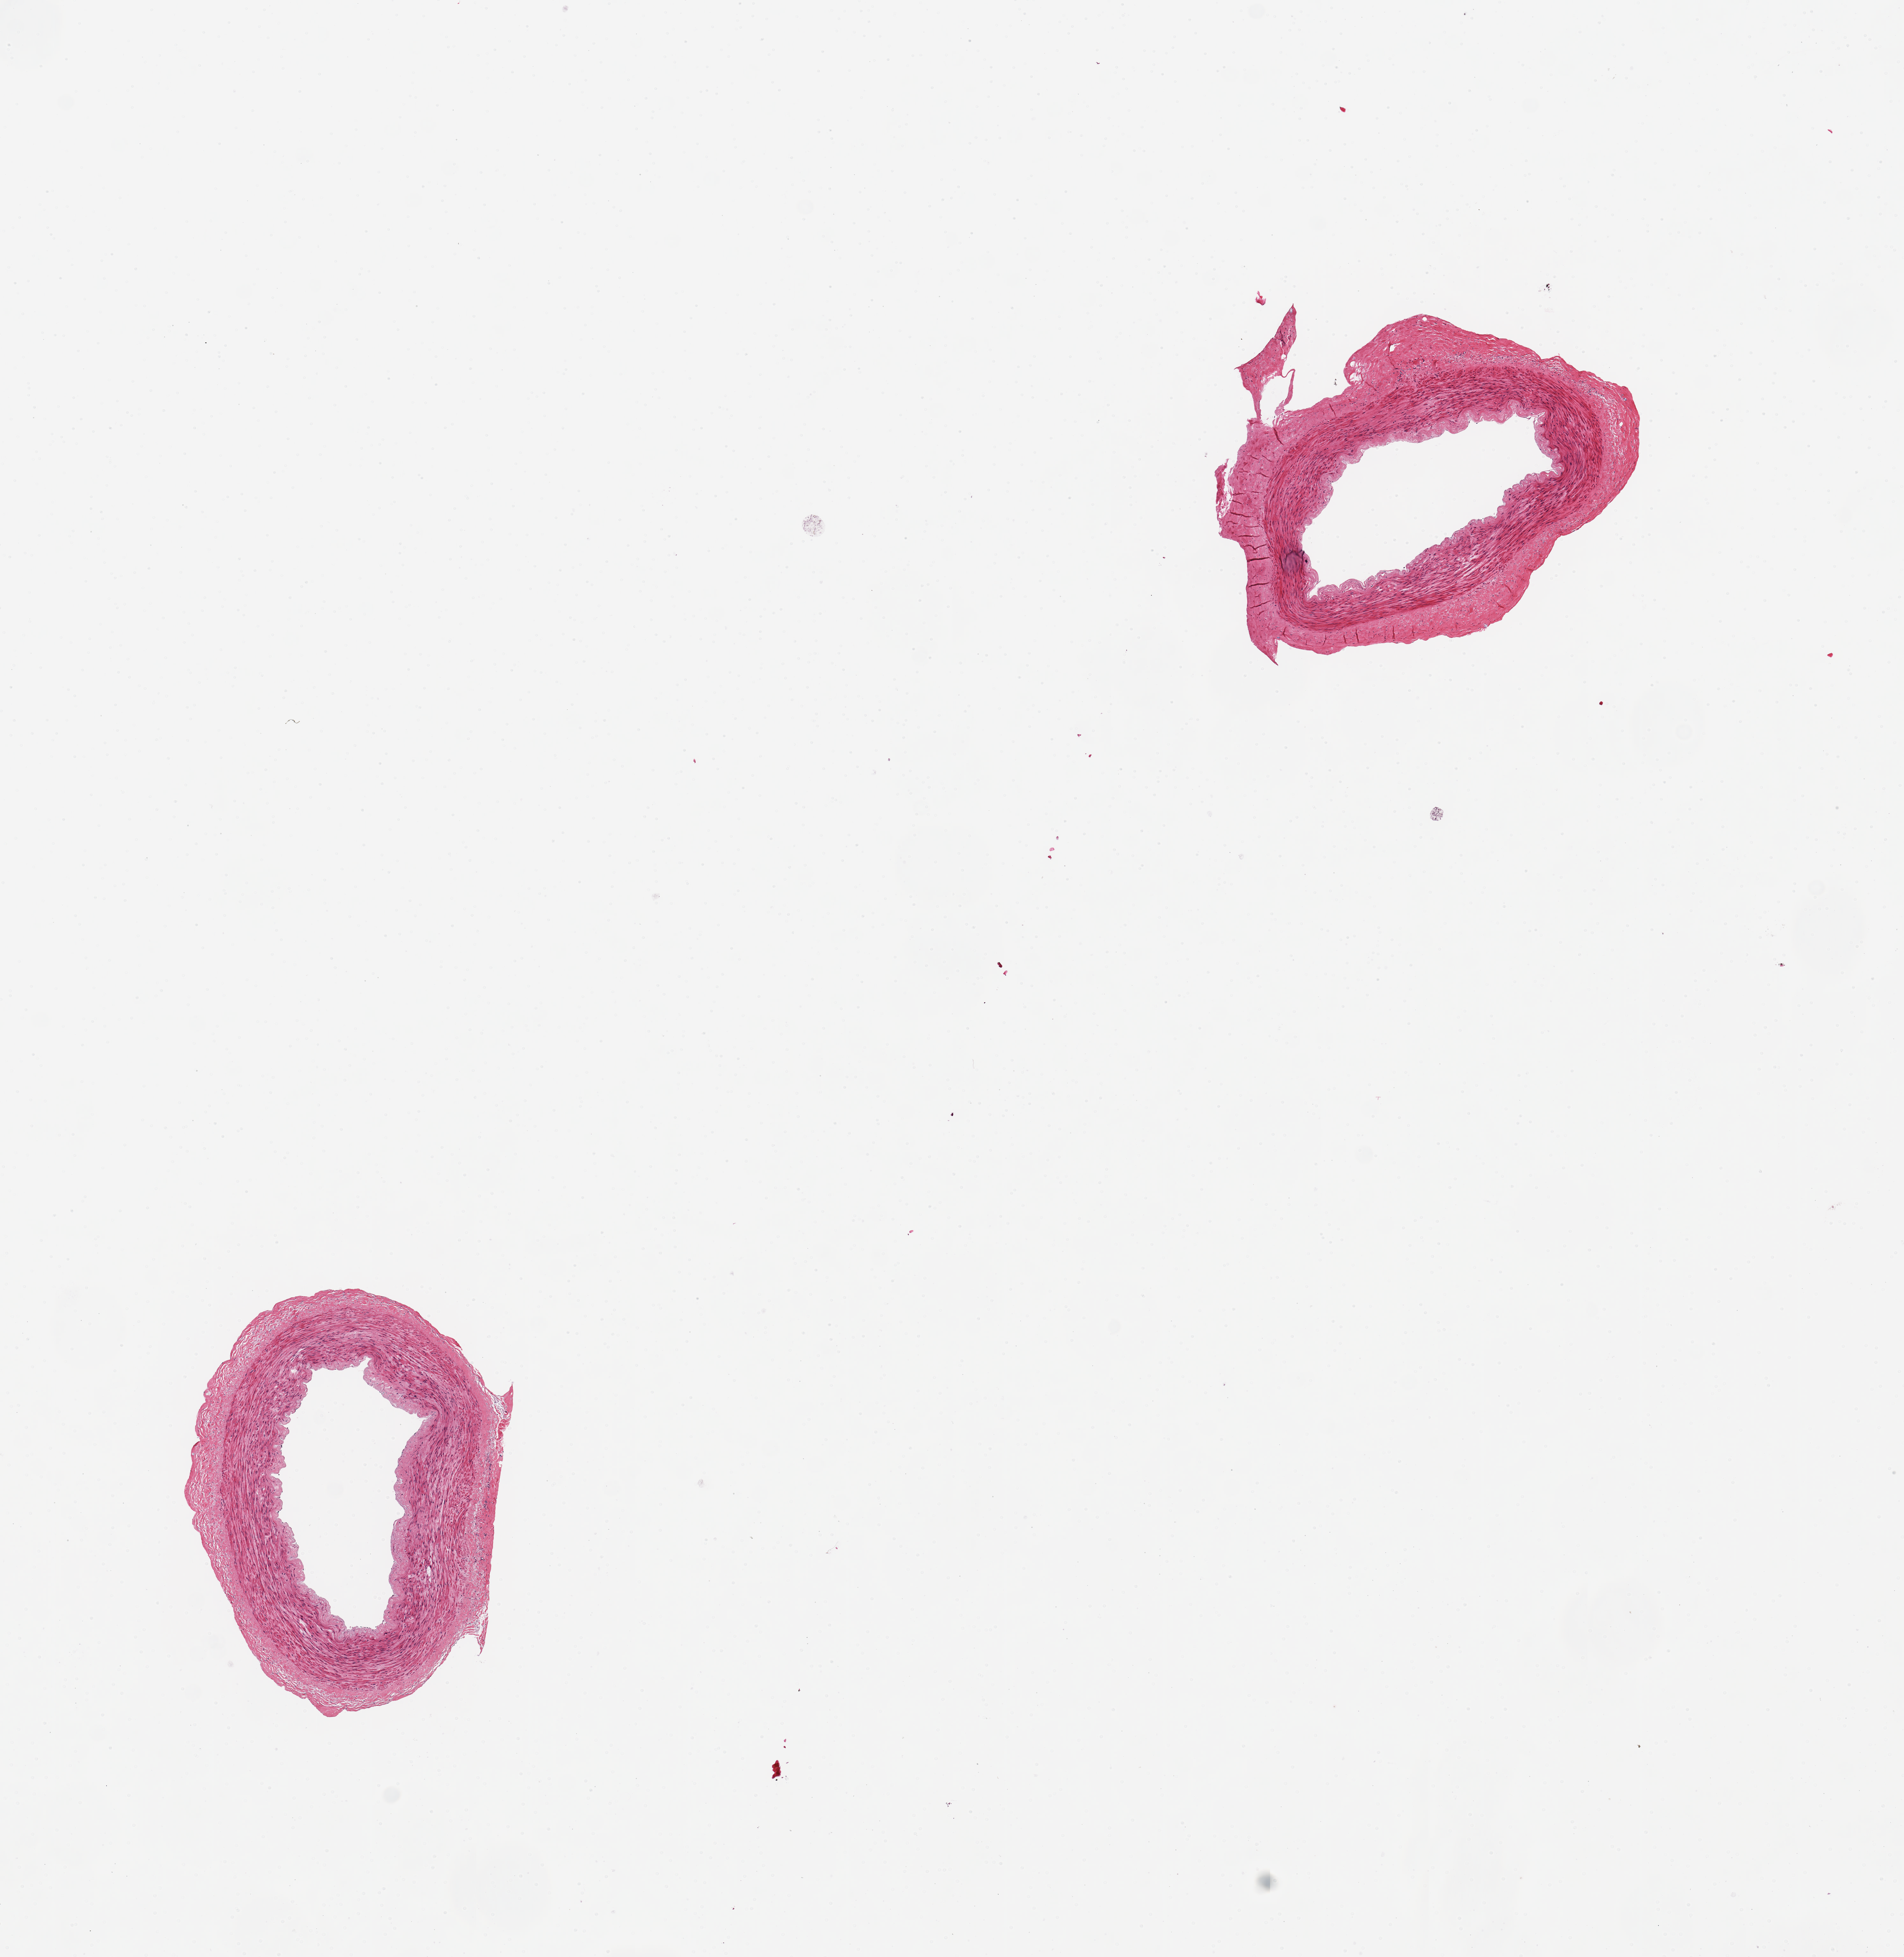
Digitized hematoxylin and eosin (H&E)-stained section — low-resolution overview of the scanned area, about 11.8 x 12.1 mm; PAXgene-fixed, paraffin-embedded tissue; target tissue: tibial artery; tissue donor sample.
Review note (as recorded): 2 pieces, 3 & 3mm in diameter; no plaques, no calcium, no extraneous adipose.